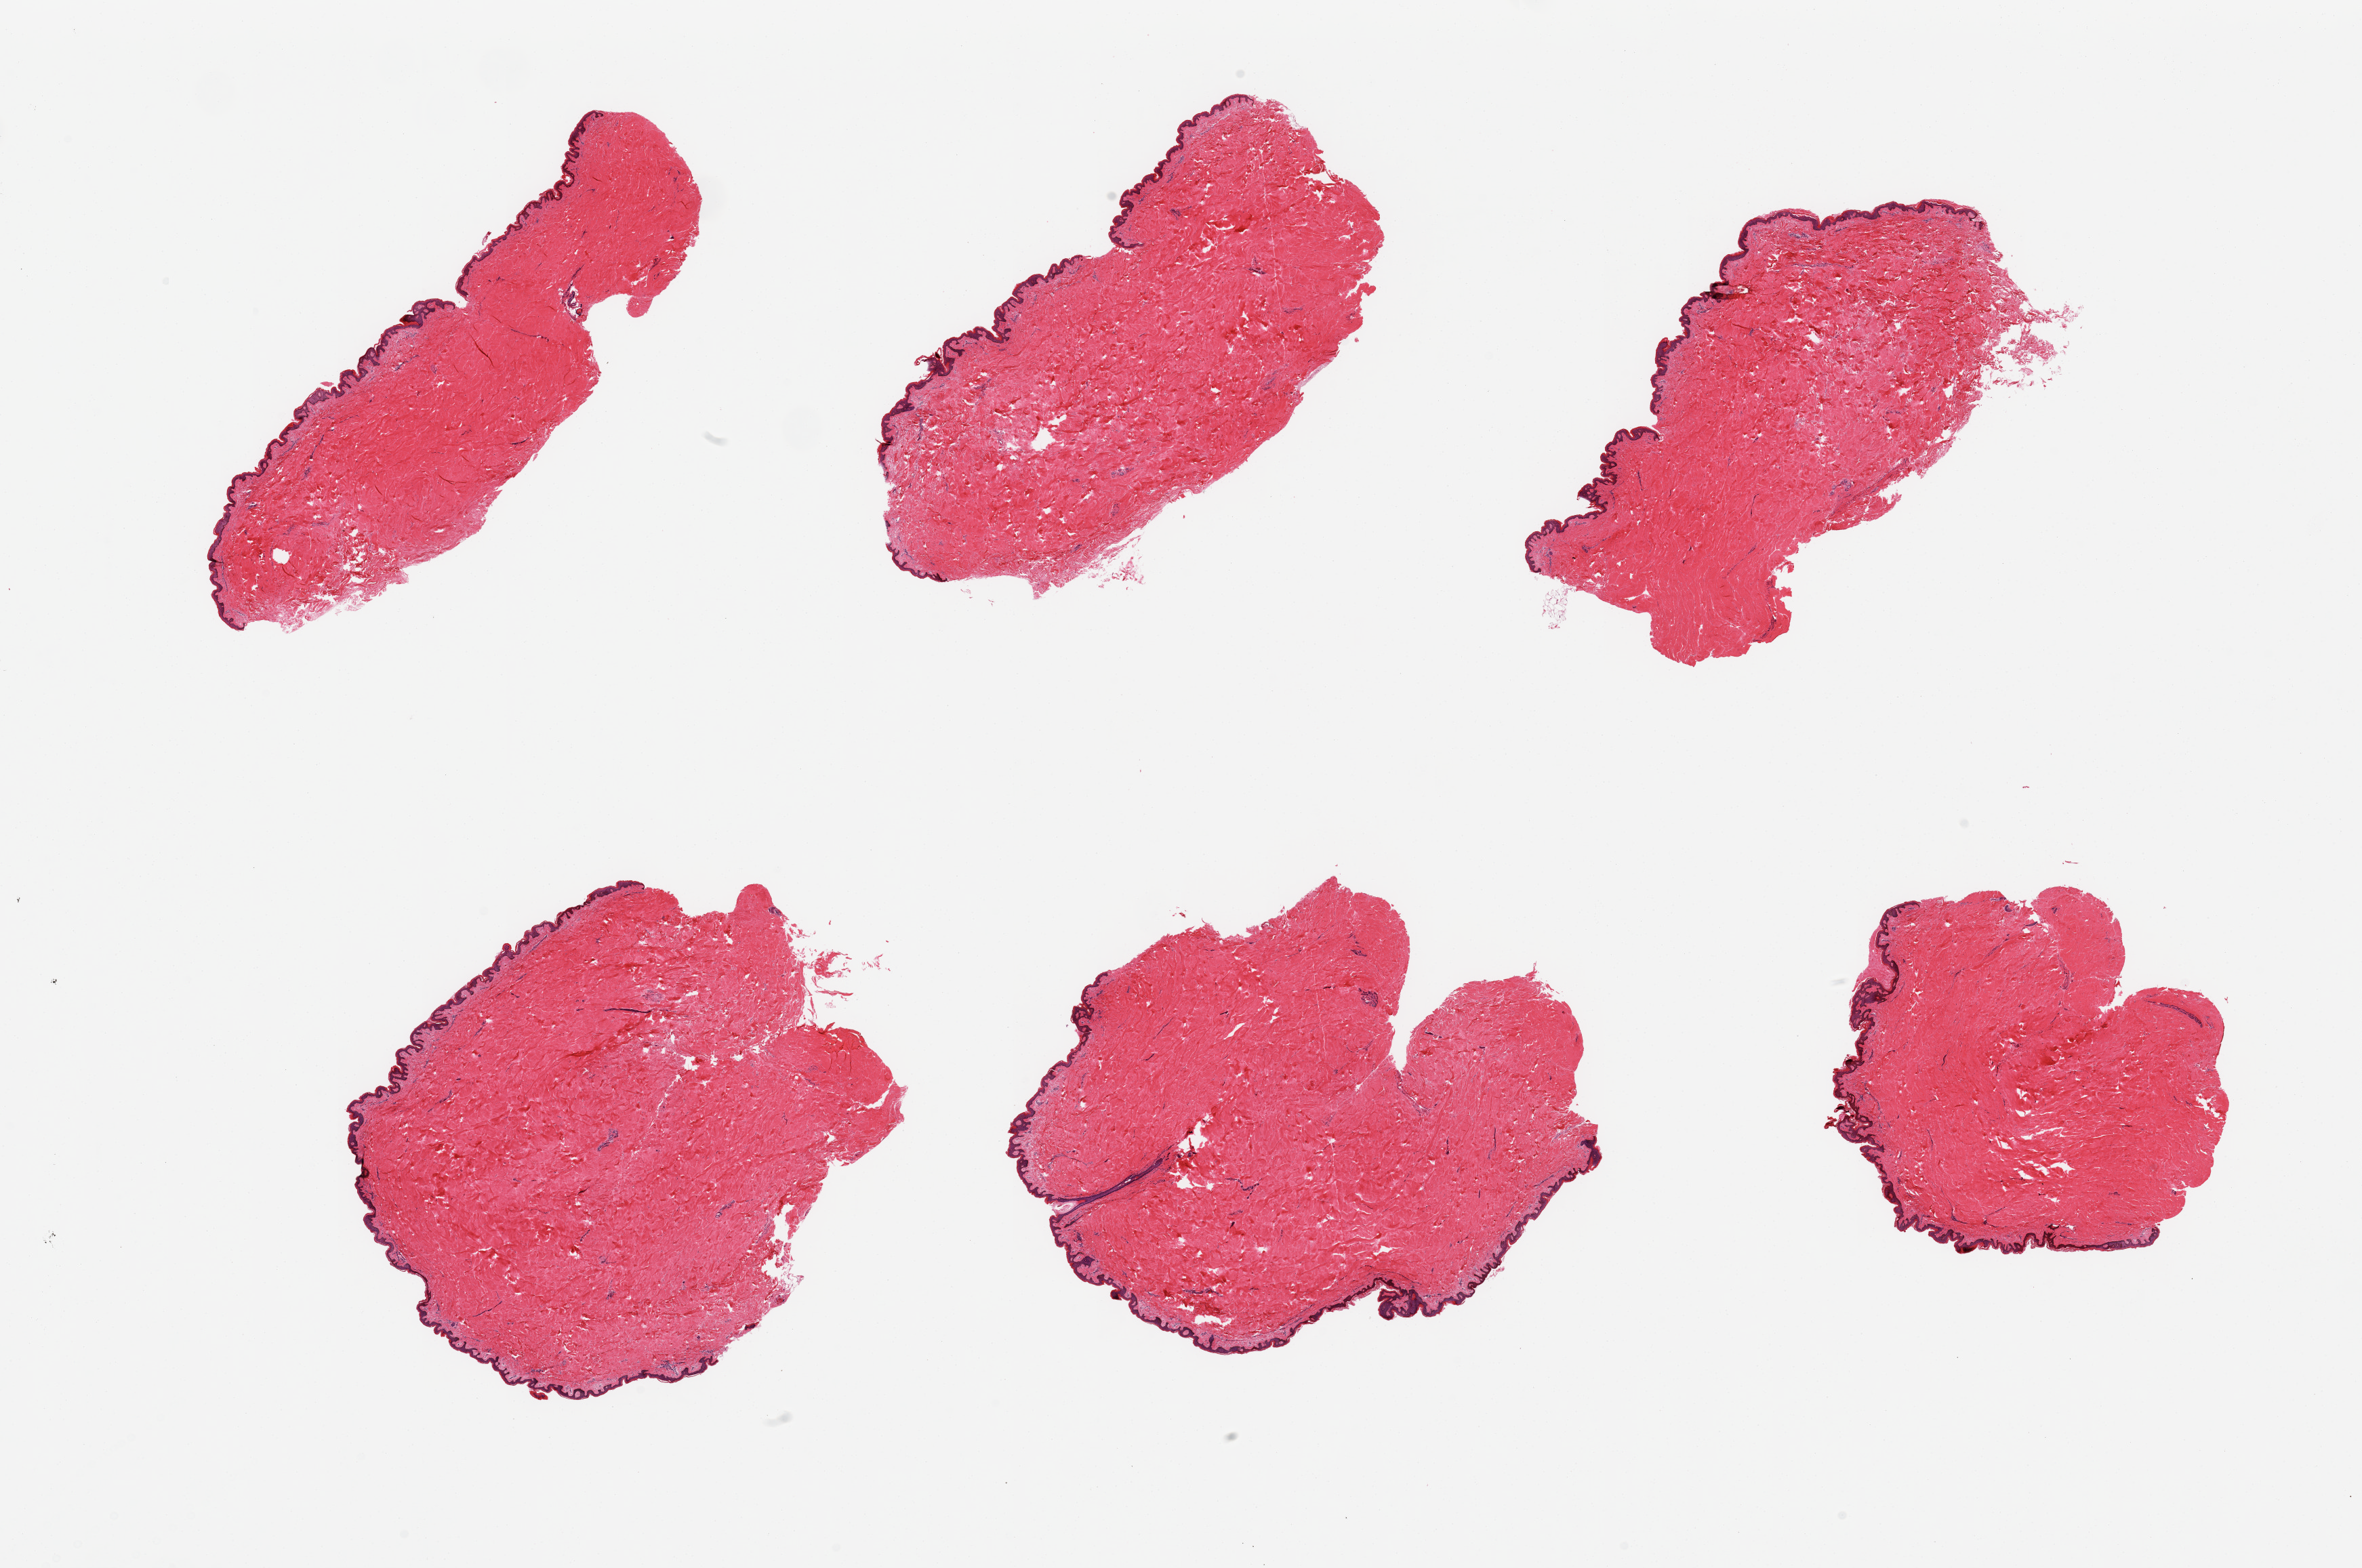
Hematoxylin and eosin (H&E) whole-slide image, whole scanned area (about 27.6 x 18.3 mm, acquisition: 20x scan) shown as a low-resolution overview. PAXgene-fixed paraffin-embedded (PFPE) section. Section of skin of suprapubic region (target tissue). Tissue donor sample.
* review note (as recorded): 6 pieces; well trimmed; free of intrademal fat and hair